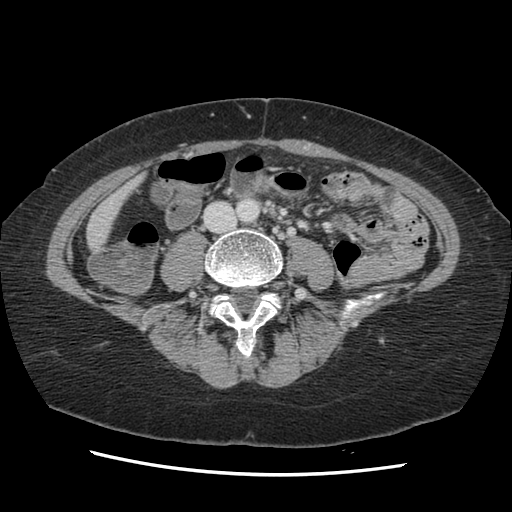
Contrast-enhanced abdominal CT, one axial slice; position 16 of 141 along the scan axis; soft-tissue window (W 400 / L 40 HU); 2.5 mm slice thickness; 512 × 512 image matrix. Female patient, age 61 years. Case-level facts recorded for this patient, not image findings: diagnosis: colorectal cancer liver metastases, imaged before liver resection; multiple liver metastases: no; largest metastasis: 2.4 cm; disease in both lobes: no.
Annotated regions visible in this slice (outlined manually by an expert reader):
- liver: bounding box (x1, y1, x2, y2) in pixels: (88, 178, 140, 248)
- planned liver remnant (the part of the liver to remain after resection): (88, 178, 141, 249)